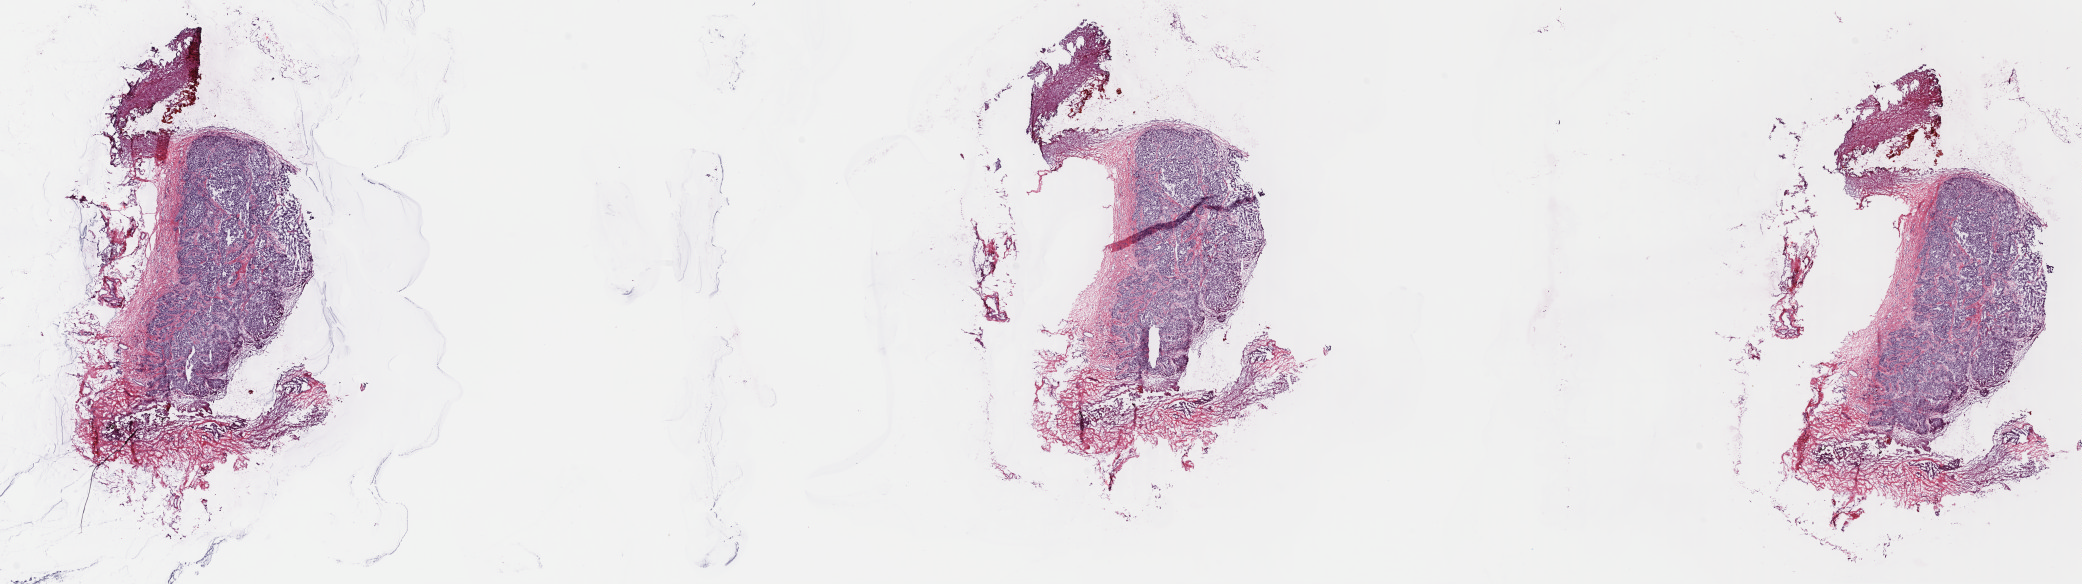
Digitized H&E-stained tissue section (whole slide), whole scanned area (about 32.7 x 9.2 mm, acquisition: 40x scan) shown as a low-resolution overview, frozen section, mesothelium, primary tumour sample. Patient: male, age at initial diagnosis 73 years. Composition of this section per pathologist review: tumour cells 80%, tumour nuclei 95%, normal cells 0%, stromal cells 20%, necrosis 0%. Infiltration values recorded for this section: lymphocyte infiltration 0%, monocyte infiltration 0%, neutrophil infiltration 0%.
- AJCC pathologic stage: III (7th edition)
- TNM: T1b N2 M0
- histologic diagnosis: Epithelioid mesothelioma, malignant (pleura, NOS)